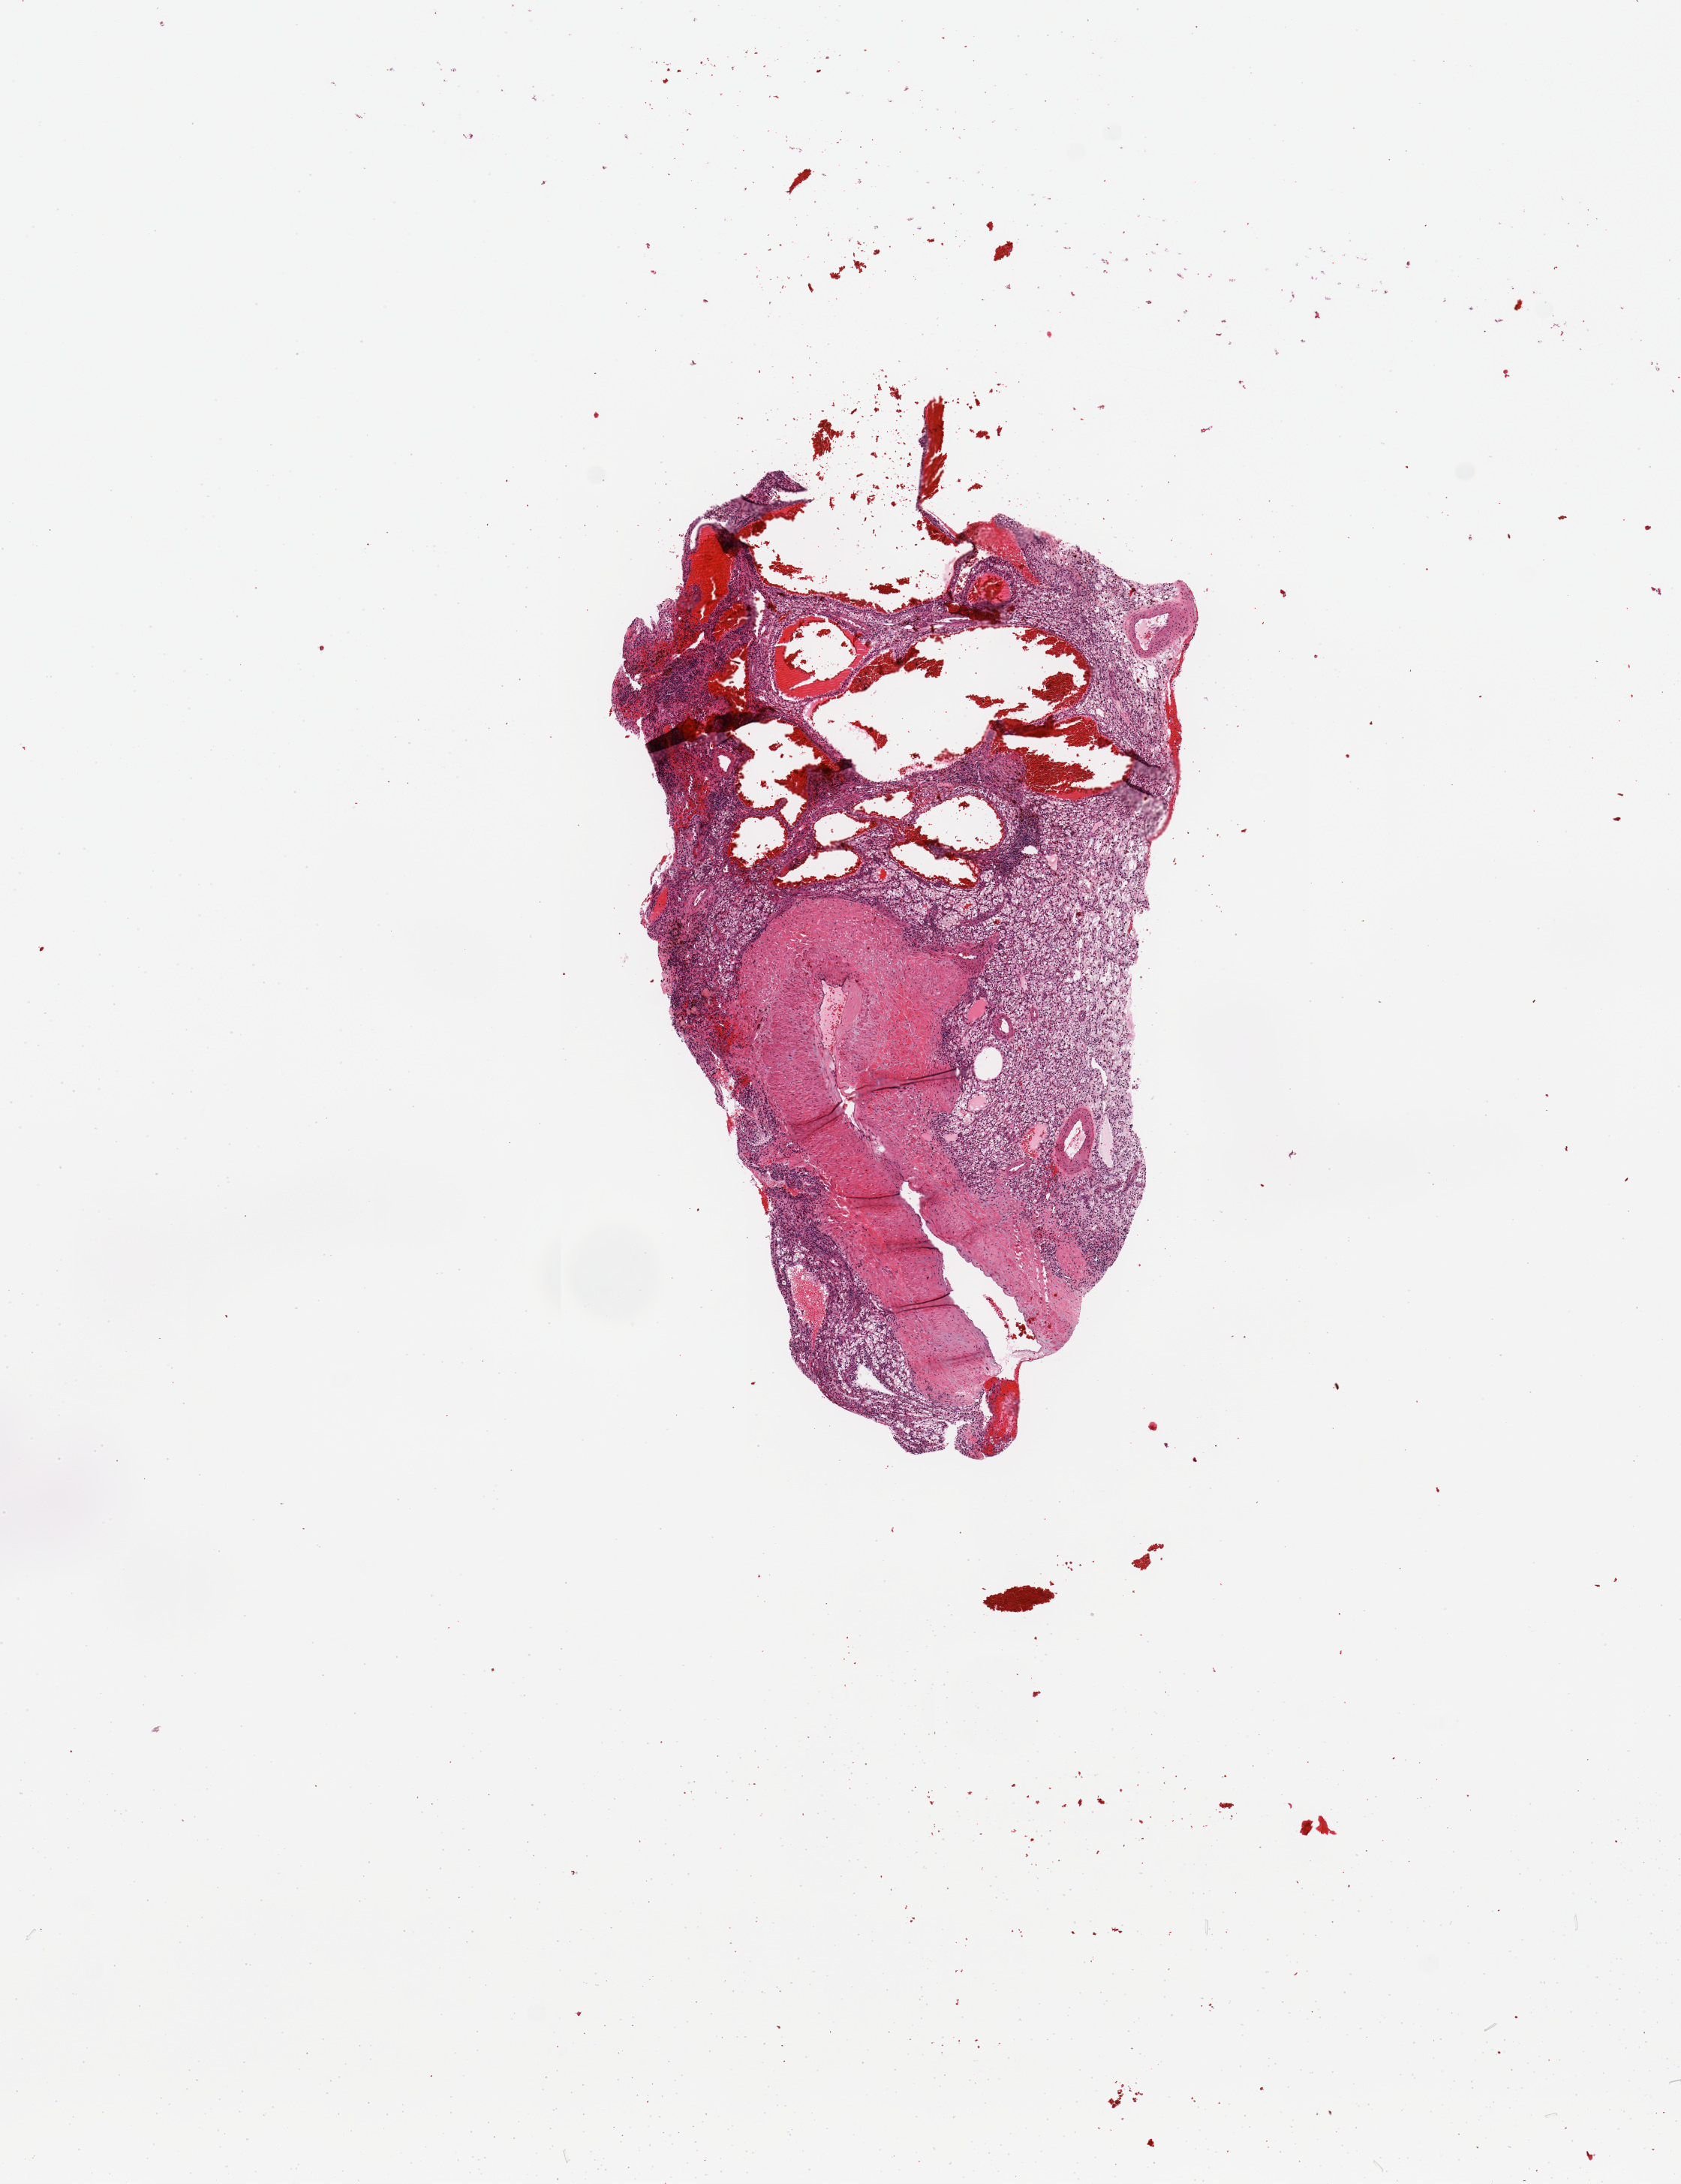
Digitized Hematoxylin and eosin (H&E) stained tissue section (whole slide) — shown as a low-resolution overview of the whole scanned area (about 8.9 x 11.5 mm, acquisition: 20x scan), tumour tissue sample, kidney. Male, 67 y/o. Histologic grade: G2 (moderately differentiated).
Histologic diagnosis: Renal cell carcinoma, NOS. AJCC pathologic stage: I. Primary tumour site (as recorded): lower pole.